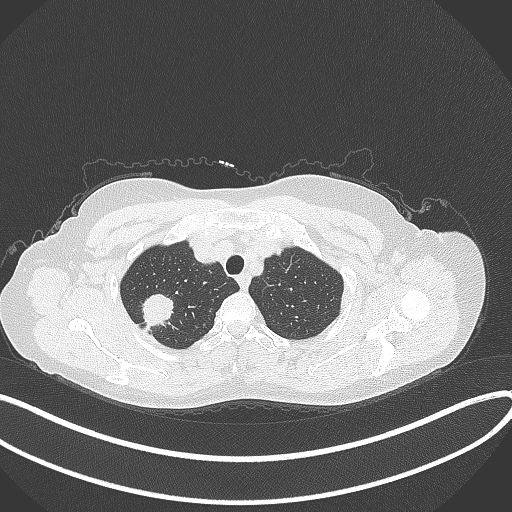
Chest CT, one axial slice. Slice 312 of 337 in the series (ordered by position). Reconstruction kernel B70f. Lung window (W 1500 / L -600 HU). 1 mm slice thickness. 512 × 512 image matrix, field of view 400 × 400 mm. Patient: female, 50 years. Case-level facts recorded for this patient, not image findings: clinical TNM (as recorded): T1c N0 M0.
Outlined on this slice (rectangle marked by the reading radiologist):
- lung tumour (recorded histology: adenocarcinoma): bounding box <137,293,178,329> (left, top, right, bottom; pixels)